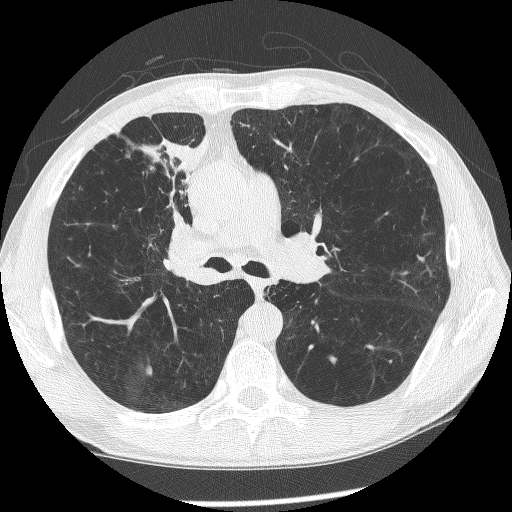
Chest CT (low-dose screening protocol), one axial image; baseline screening round; lung window (W 1500 / L -600 HU); 120 kVp; slice 148 of 266 in the series; 512 × 512 image matrix, field of view 340 × 340 mm. Male participant, aged 60 years at enrolment. Current smoker at enrolment.
Expert-annotated lung lesion, bounding box <145,194,221,287> (left, top, right, bottom; pixels). The exam's reader record, not a measurement of the box and not confirmed to be the same lesion: non-calcified nodule or mass ≥4 mm, right upper lobe, 12 × 8 mm, spiculated (stellate) margins, mixed attenuation. Official screen result: positive, change unspecified: nodule(s) >= 4 mm or enlarging nodule(s), mass(es), or other non-specific abnormalities suspicious for lung cancer. Later outcome: lung cancer diagnosed 208 days after this screen — squamous cell carcinoma, NOS, right upper lobe, right middle lobe, right main stem bronchus, poorly differentiated (G3), stage IV (AJCC 6th edition).